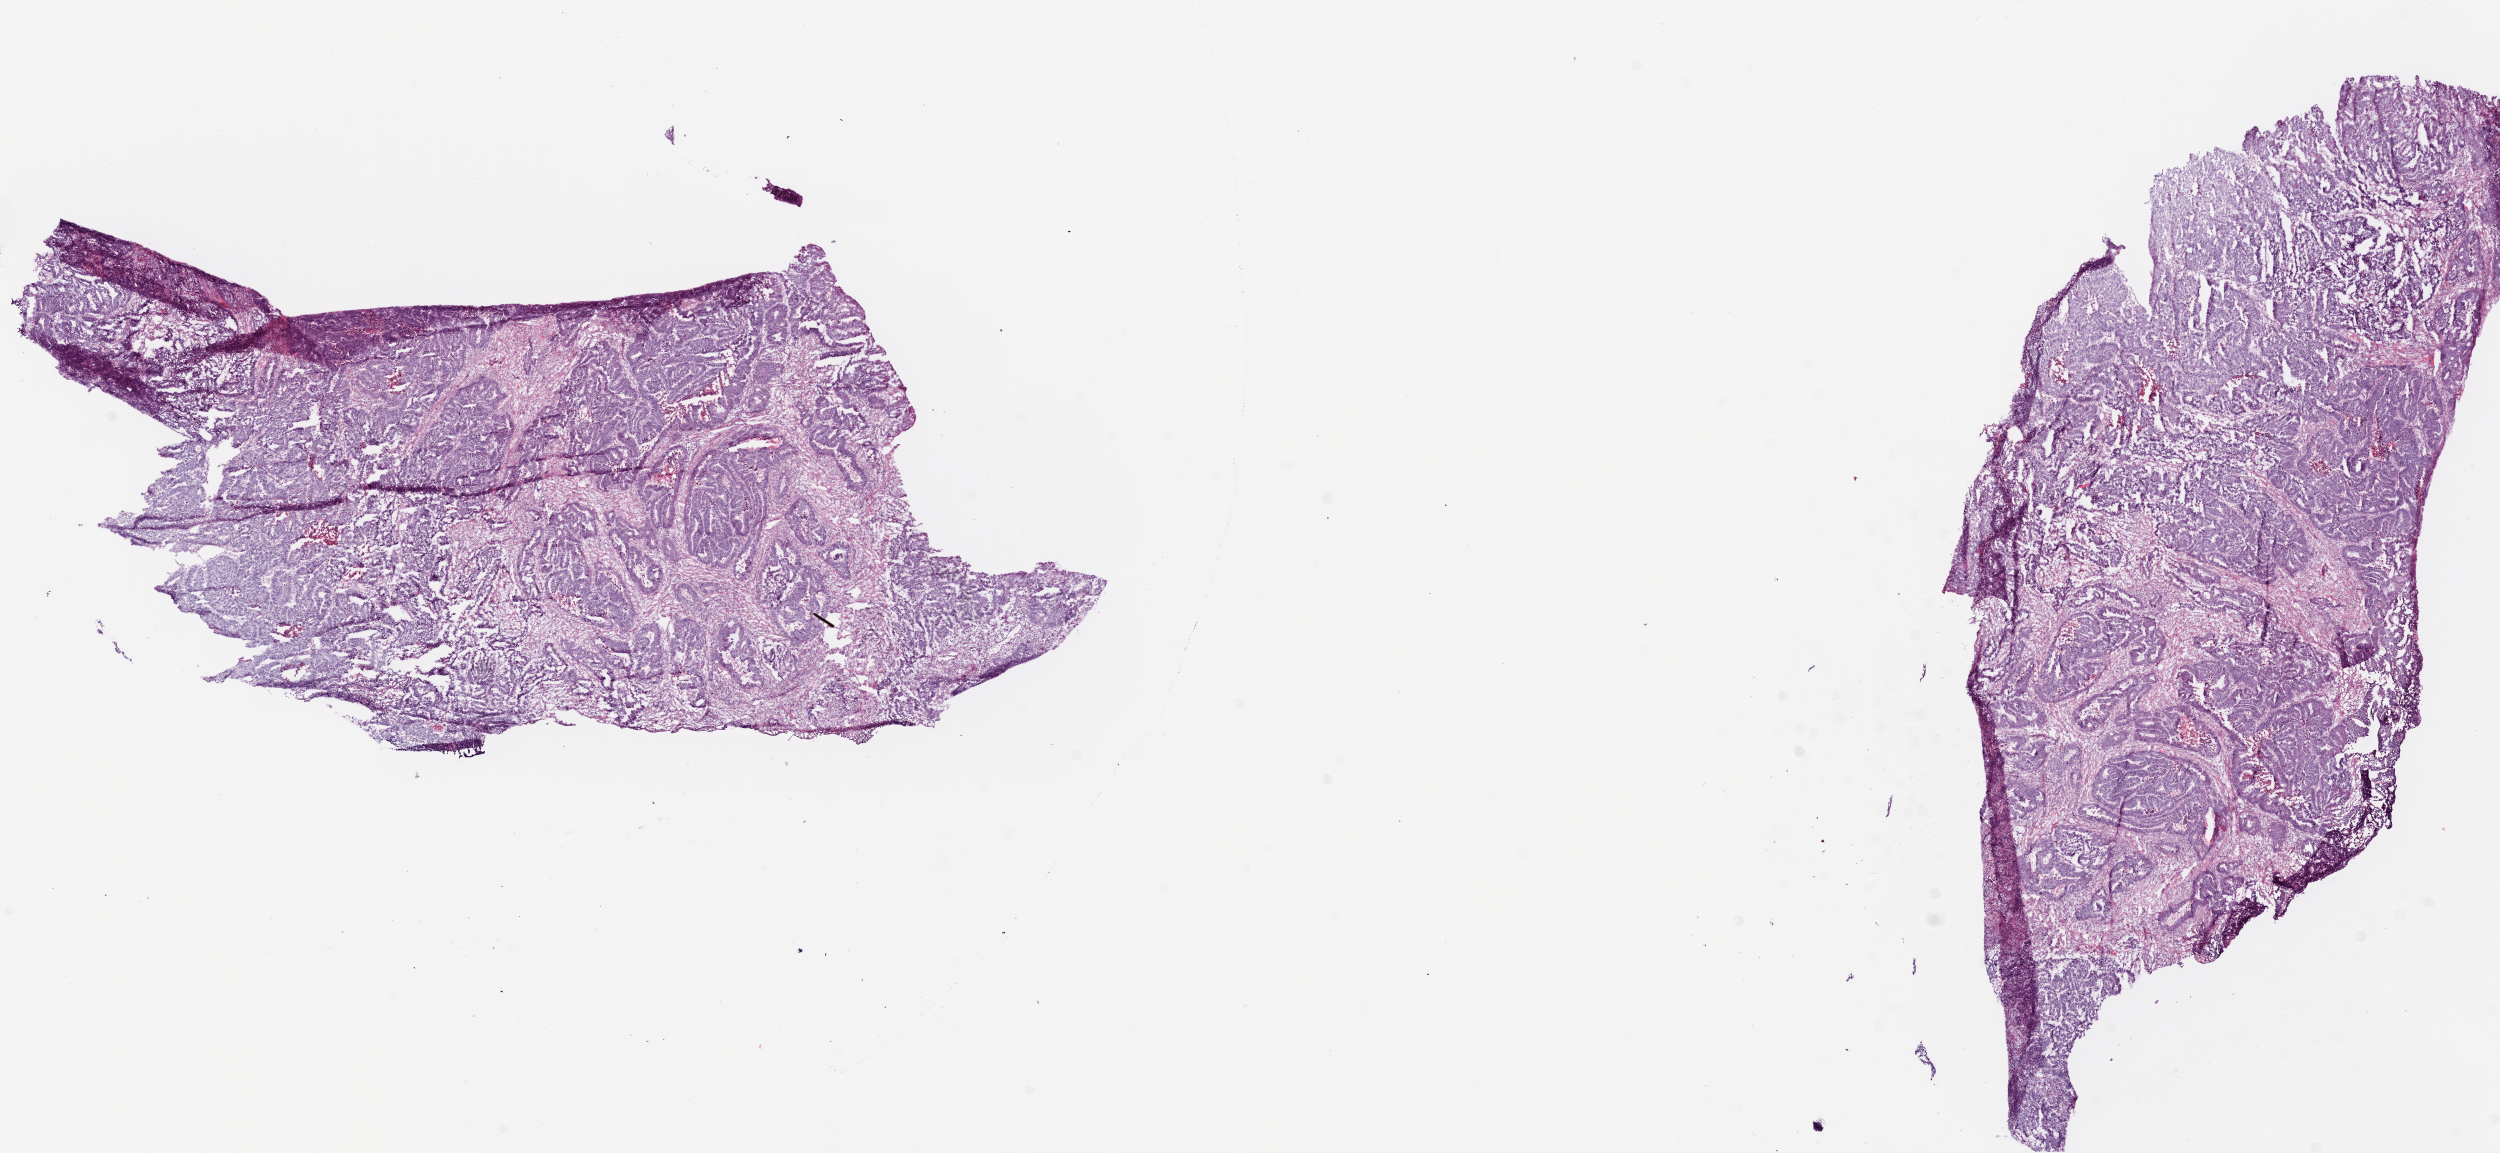
Whole-slide histology image, H&E-stained — shown as a low-resolution overview of the whole scanned area (about 20.1 x 9.3 mm, acquisition: 20x scan). Frozen section from the bottom of the tissue portion. Primary tumour sample from the rectum. Male patient; age at initial diagnosis 65 years. Slide review estimates, as recorded: tumour cells 78%, tumour nuclei 80%, normal cells 0%, stromal cells 12%, necrosis 10%.
Pathologic diagnosis: Adenocarcinoma, NOS. AJCC pathologic stage: I.